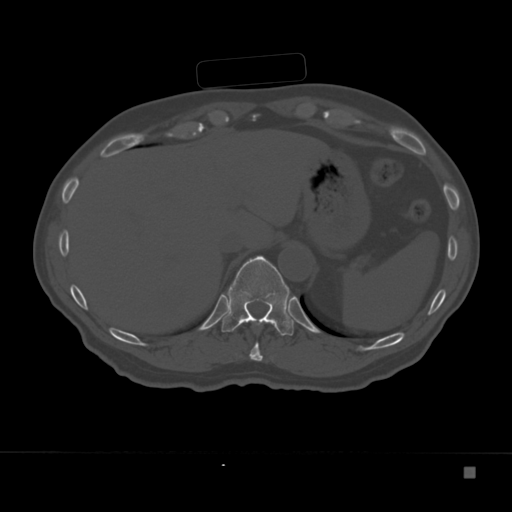
CT including the spine, one axial slice; position 158 of 332 along the scan axis; reconstruction kernel Br40s; 120 kVp; bone window (W 1800 / L 400 HU); 1.5 mm slice thickness; 512 × 512 image matrix, field of view 389 × 389 mm. Patient: male, 72 years. Case-level facts recorded for this patient, not image findings: primary cancer: skeletal.
Structures marked on this image (semi-automatically segmented with operator editing):
- T10 vertebra: box from (x=249, y=342) to (x=263, y=361) px
- T11 vertebra: (x=222, y=256)–(x=294, y=336)